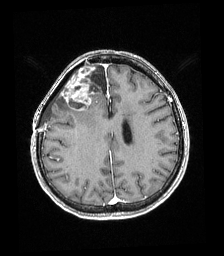
Brain MRI from a brain-tumour surgery series, one axial slice. Slice 69 of 192 in the series (ordered by position). T1-weighted post-contrast. 1 mm slice thickness. 224 × 256 image matrix, field of view 219 × 250 mm. From the clinical record (not read from this slice): histopathology: Astrocytoma; WHO grade: 4; IDH mutation: yes; tumour location: Right superficial frontal.
Structures marked on this image (outlined manually by an expert reader):
- tumour: bounding box [x1, y1, x2, y2] px = [62, 63, 94, 111]